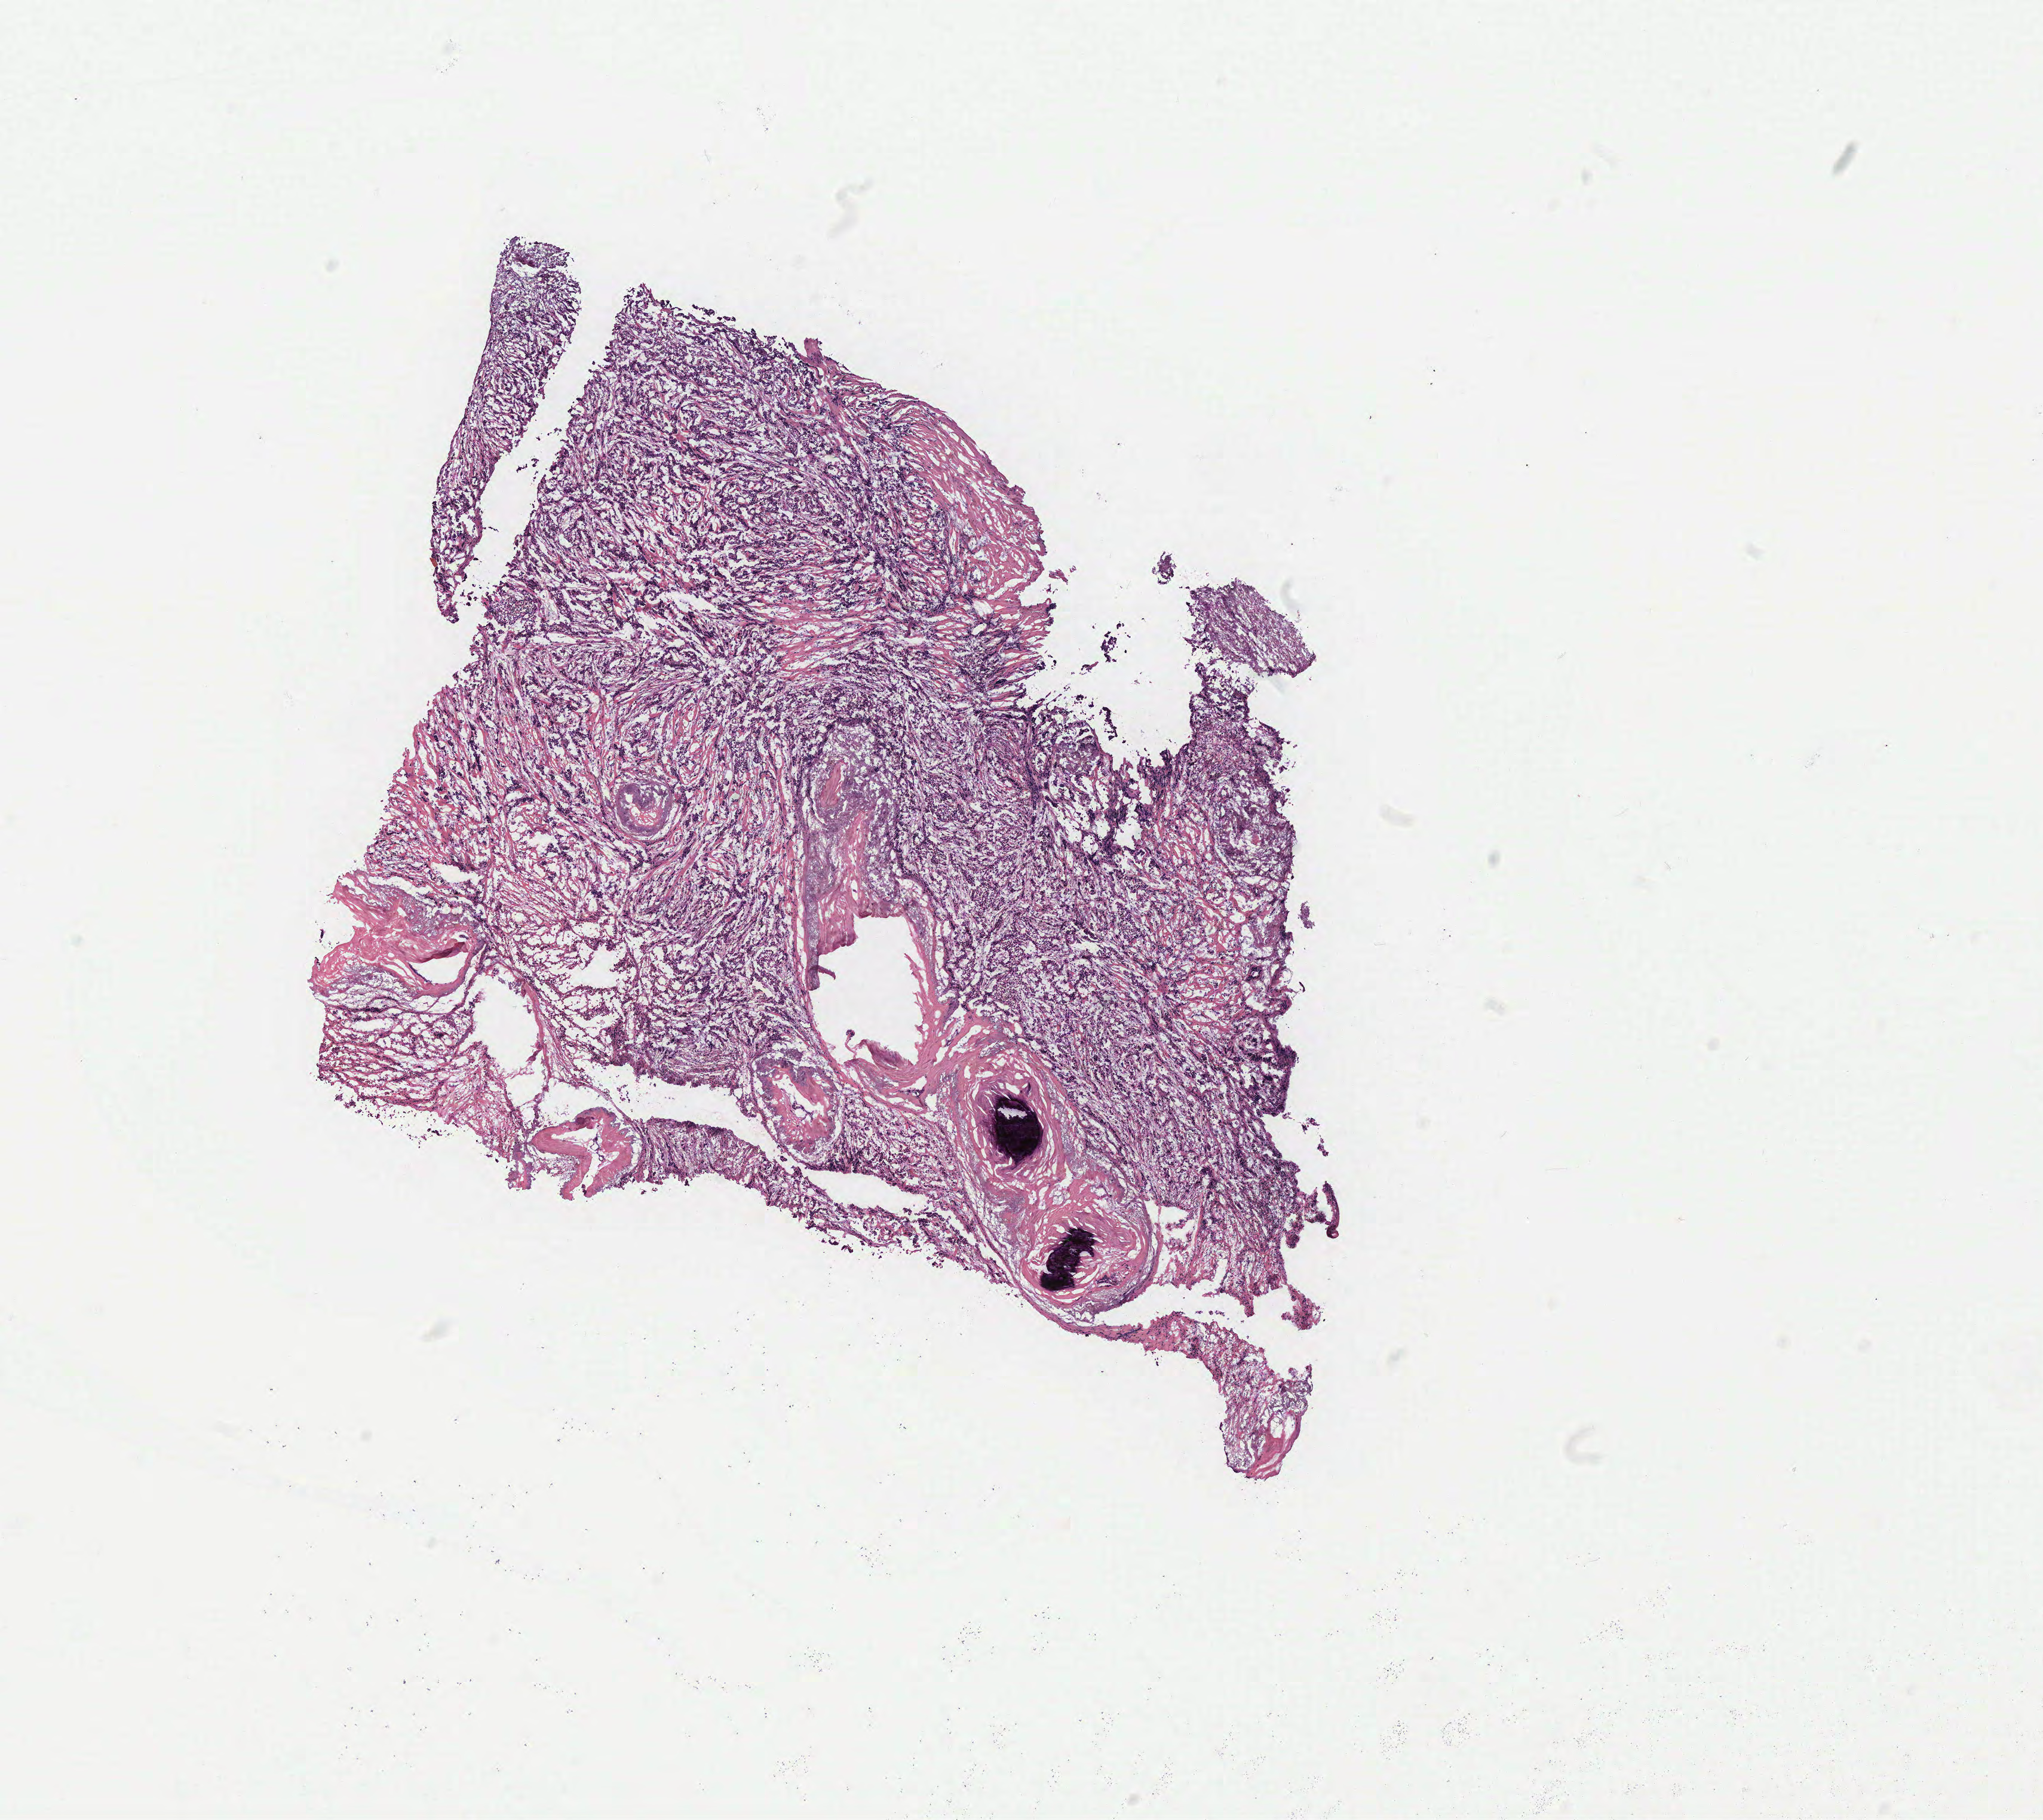
Hematoxylin and eosin (H&E) stained whole-slide image, whole scanned area (about 13.7 x 12.2 mm, acquisition: 40x scan) shown as a low-resolution overview. Patient: female, age 86 years.
Specimen: breast, tumour tissue.